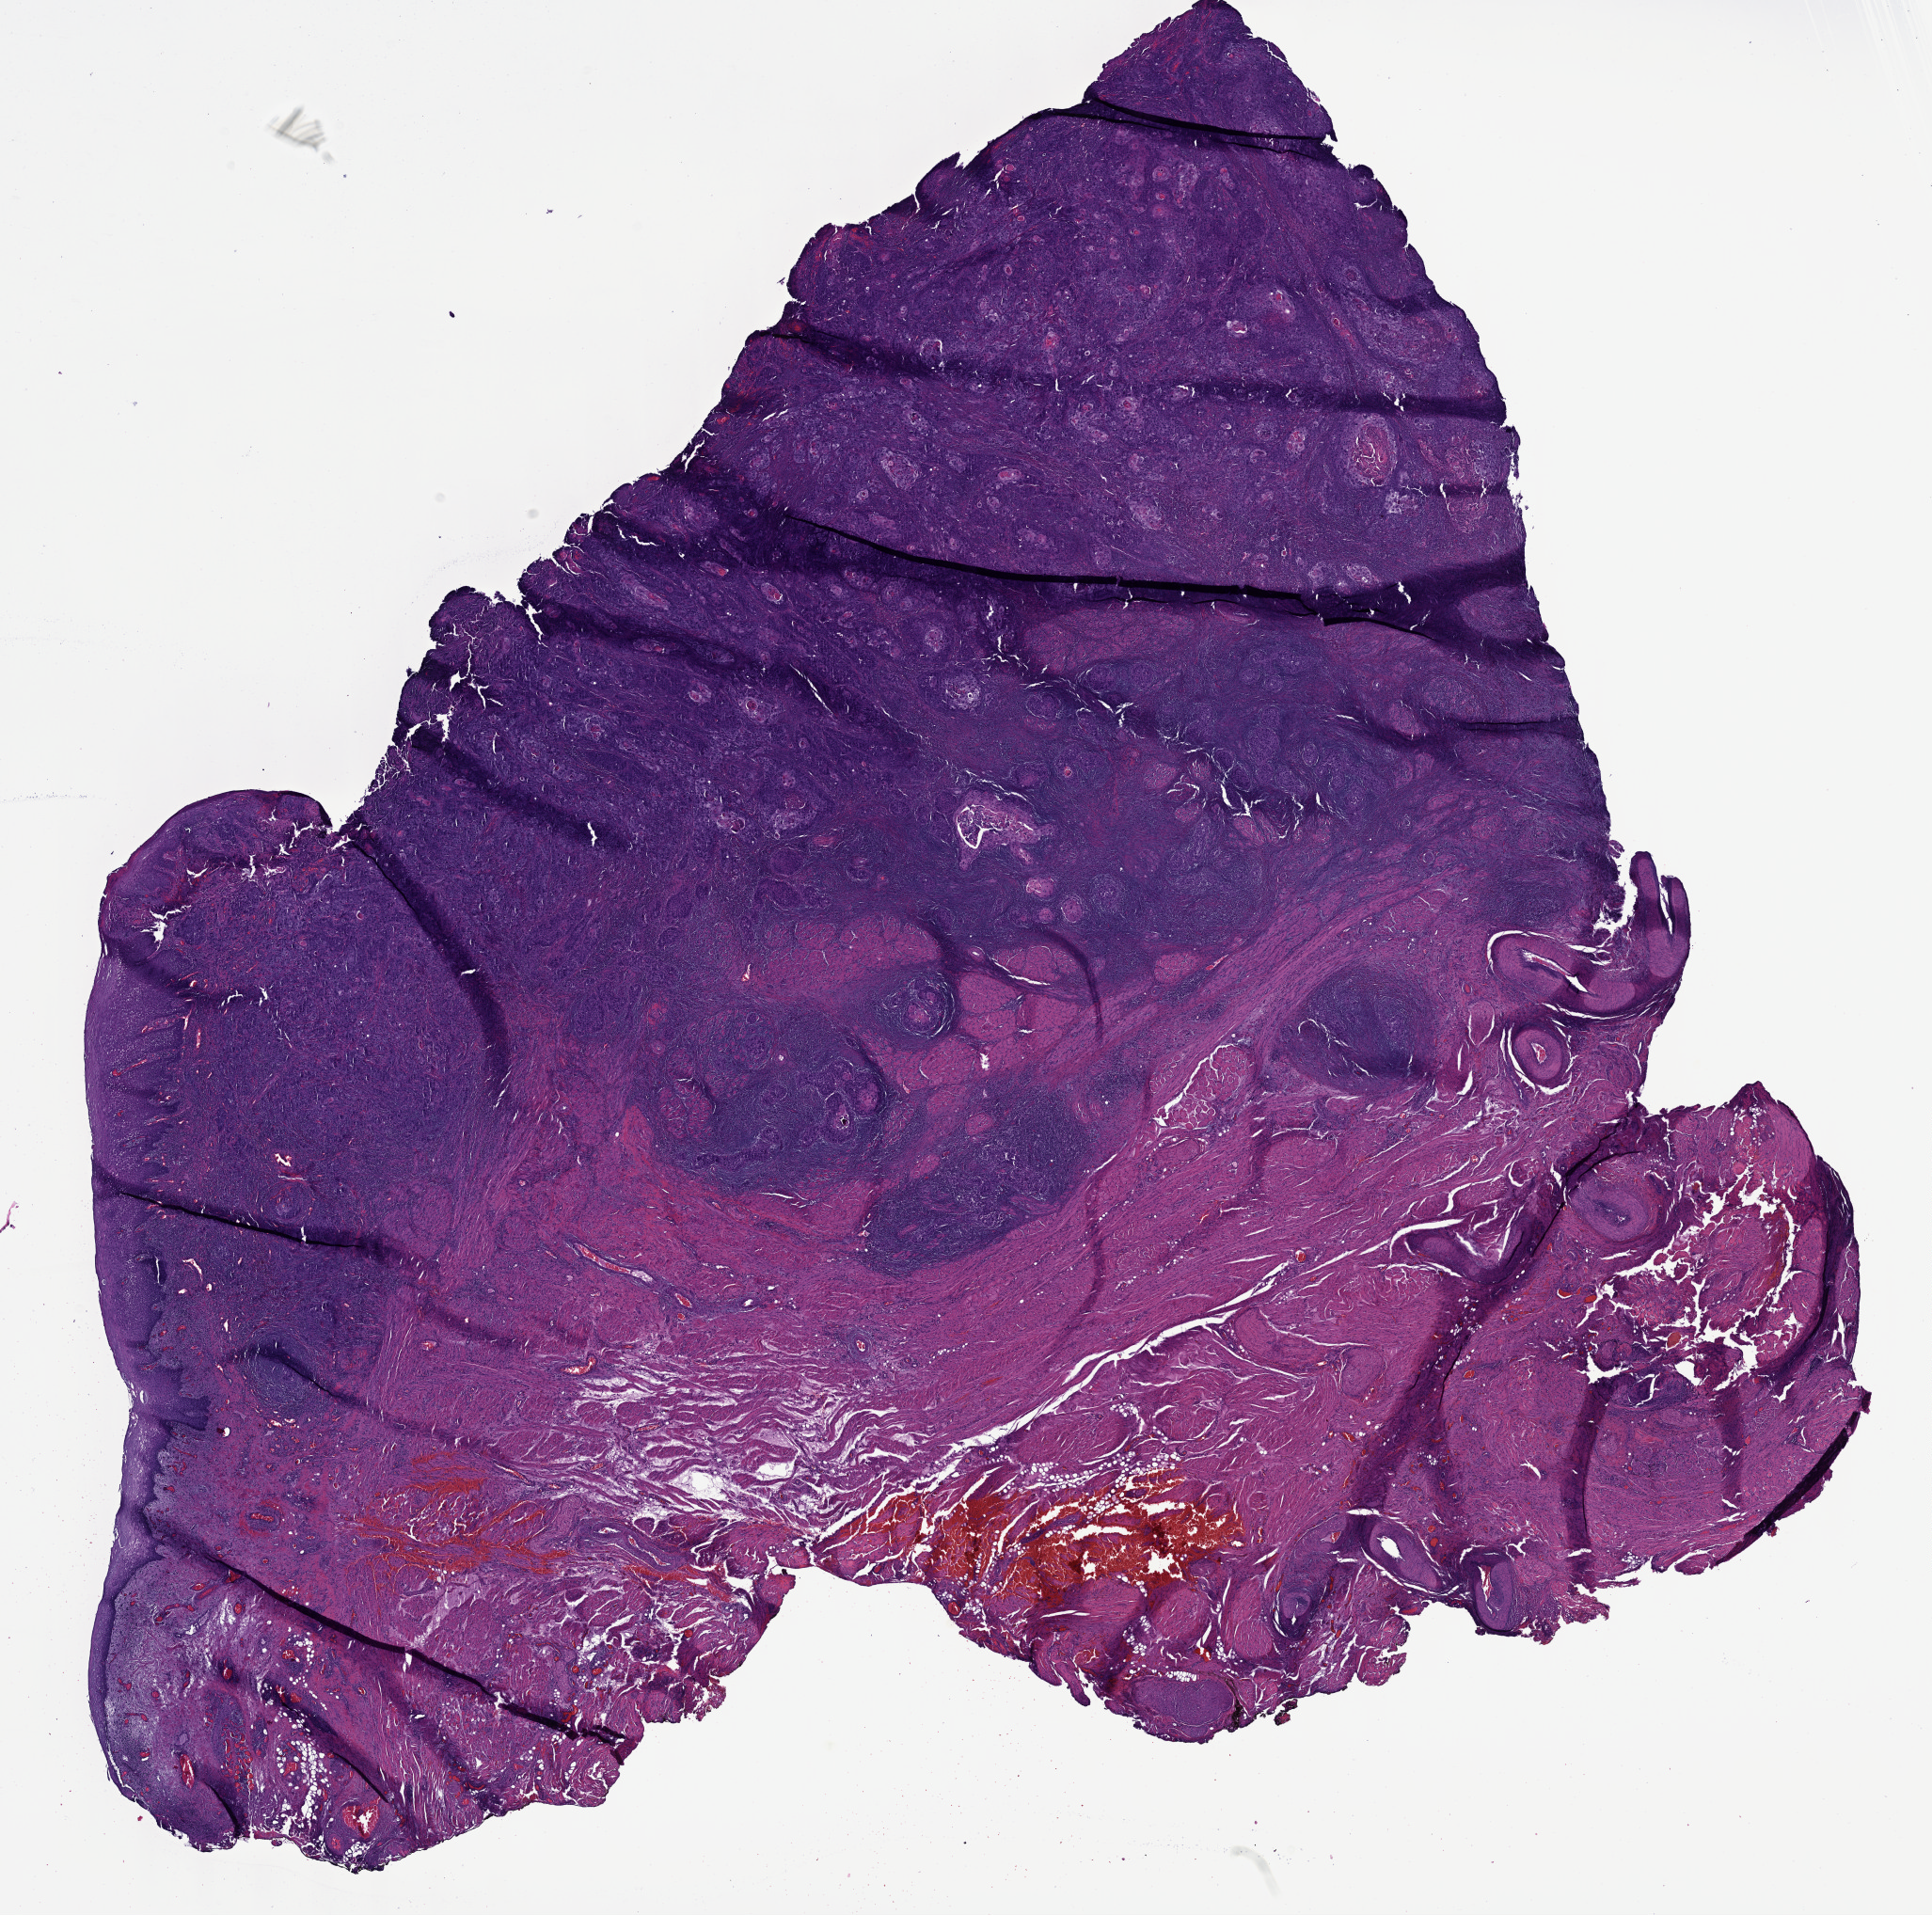
Whole-slide histology image, H&E — shown as a low-resolution overview of the whole scanned area (about 16.6 x 16.5 mm, acquisition: 40x scan), formalin-fixed paraffin-embedded (FFPE) diagnostic section, sample: primary tumour, head and neck. Female, age 50 years at initial diagnosis. Histologic grade: G2 (moderately differentiated).
Laterality: left. AJCC pathologic stage: III. Histologic diagnosis: Squamous cell carcinoma, NOS. TNM: T2 N1.